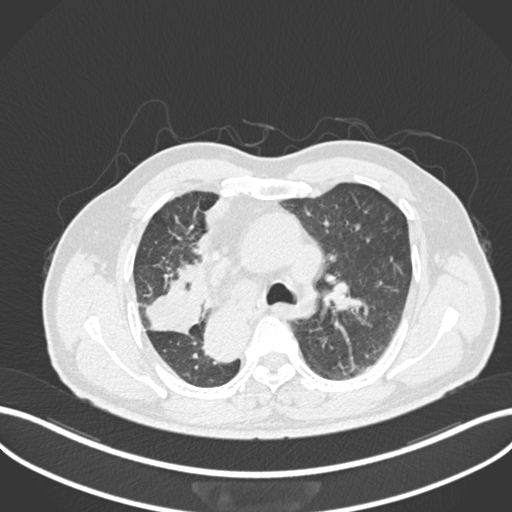
Chest CT, one axial slice. Position 159 of 206 along the scan axis. Reconstruction kernel B30f. Lung window (W 1500 / L -600 HU). 512 × 512 image matrix, field of view 400 × 400 mm. Male patient, age 67 years. Case-level facts recorded for this patient, not image findings: clinical TNM (as recorded): T2a N0 M0.
Outlined on this slice (bounding box drawn by a radiologist):
- lung tumour (recorded histology: squamous cell carcinoma): bounding box [x1, y1, x2, y2] px = [142, 275, 206, 335]